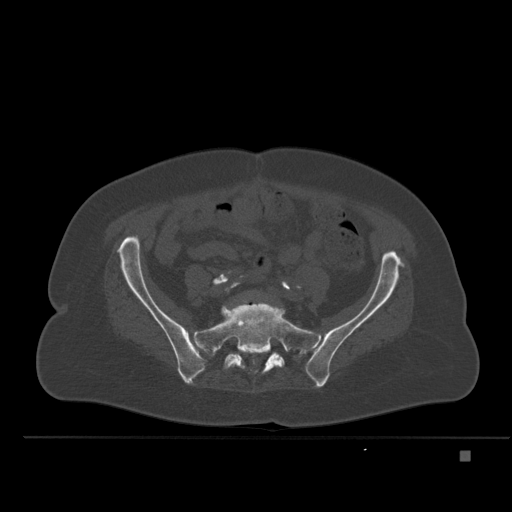
CT including the spine, one axial slice. Bone window (W 1800 / L 400 HU). 1.5 mm slice thickness. 512 × 512 image matrix, field of view 422 × 422 mm. Female patient, age 74 years. From the clinical record (not read from this slice): primary cancer: colon.
Structures marked on this image (semi-automatically segmented with operator editing):
- L5 vertebra: box from (x=249, y=294) to (x=259, y=299) px